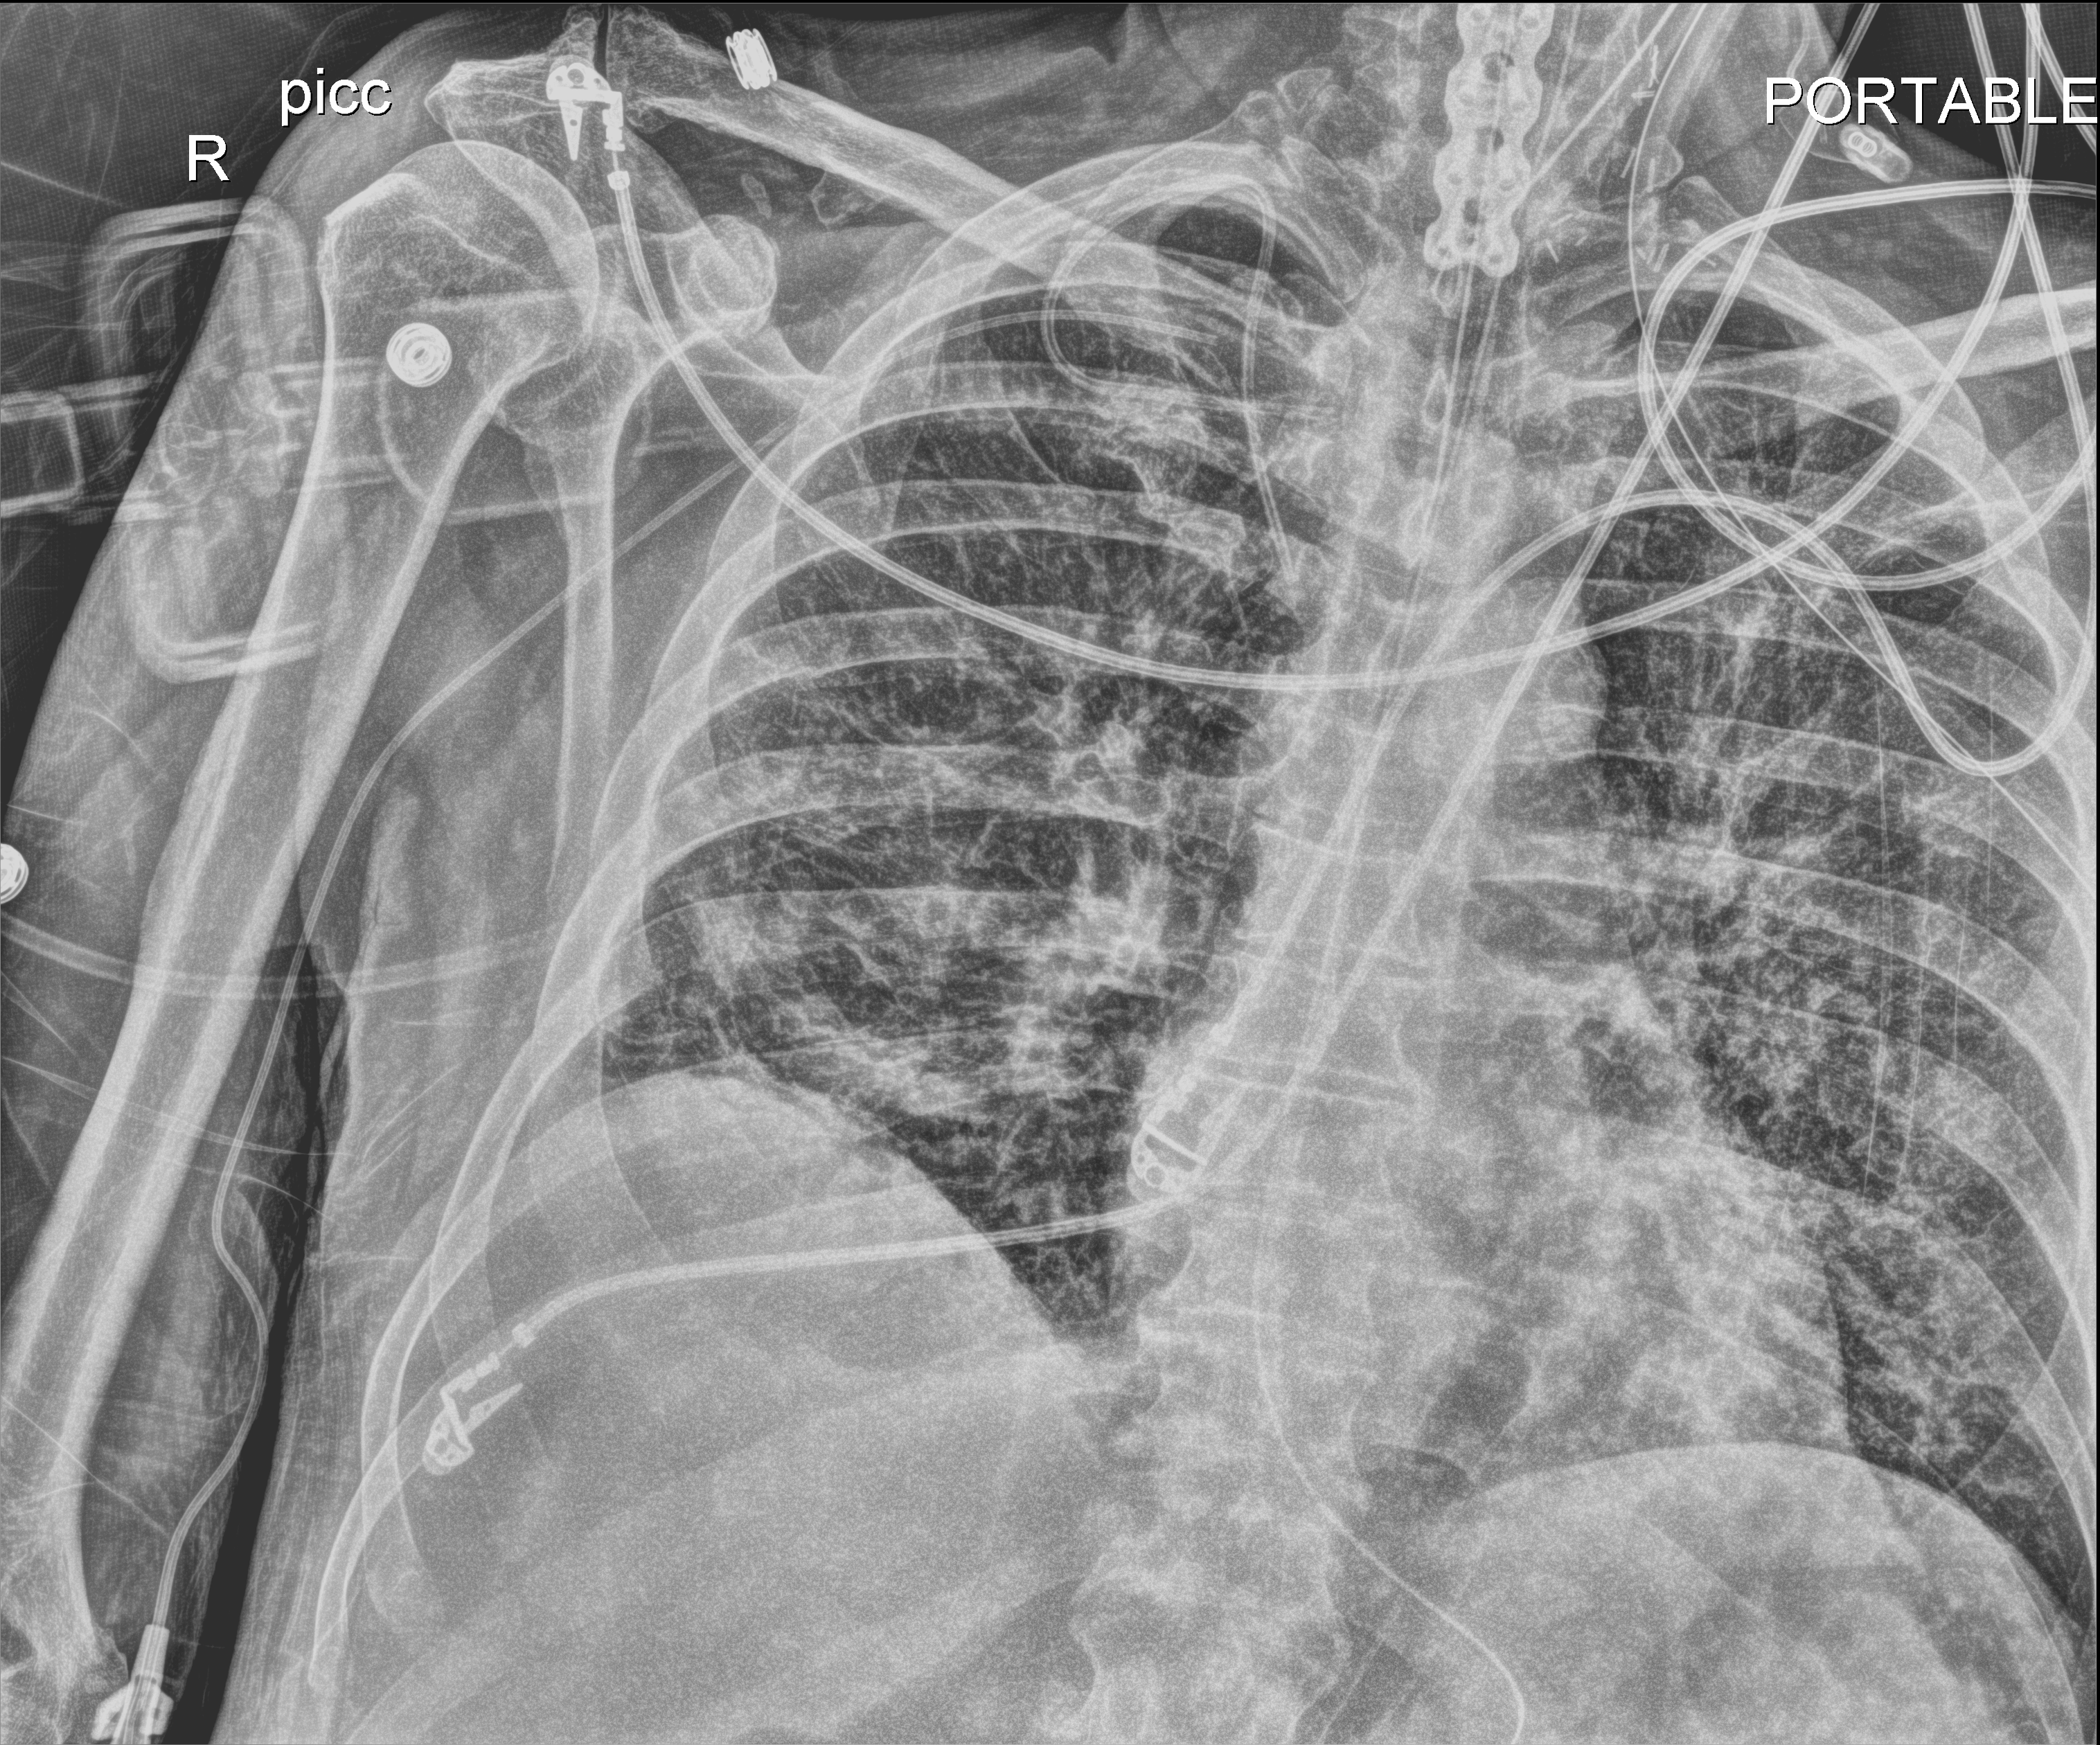
Chest X-ray (portable), anteroposterior (AP) projection. Patient hospitalised with COVID-19; male, aged 60–74 years.
Hospital-stay facts (about this admission, not read from this image; timing relative to this image not recorded):
- length of hospital stay: 43 days
- admitted to intensive care during this hospital stay: yes